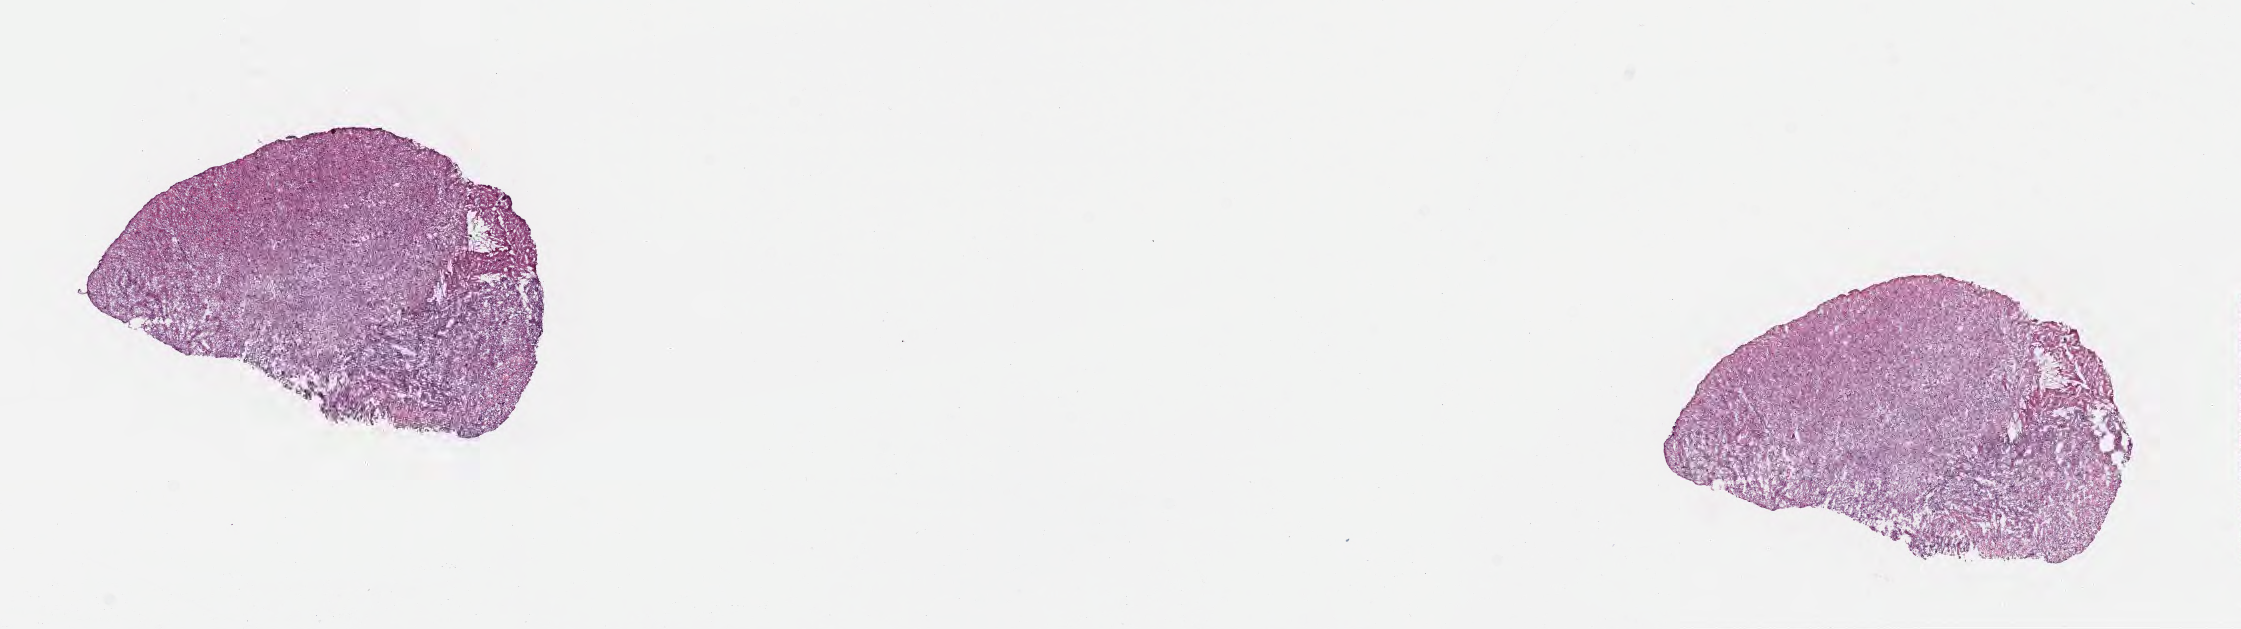
Whole-slide image, H&E stain — low-resolution overview of the scanned area, about 18.1 x 5.1 mm. Cryosection. Recurrent tumor. Site: brain. Patient: male, age at initial diagnosis 66 years. Slide review estimates, as recorded: tumor cells 71%, tumor nuclei 89%, stromal cells 18%, necrosis 2%, normal cells 9%. Inflammatory infiltration, as recorded: lymphocyte infiltration 0%, monocyte infiltration 0%, neutrophil infiltration 0%.
- section: top of the tissue portion
- patient diagnosis: Glioblastoma, NOS